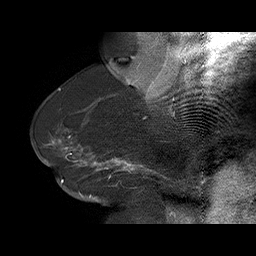
Breast MRI (dynamic contrast-enhanced), one sagittal slice; position 44 of 75 along the scan axis; dynamic contrast-enhanced series, time point 2 of 6 at this slice position (early post-contrast); 1.5 T; TE 4.5 ms, TR 32.4 ms; 256 × 256 image matrix. Female patient. From the clinical record (not read from this slice): setting: breast cancer imaged before/during neoadjuvant chemotherapy; receptor status: HR-positive, HER2-negative.
Structures marked on this image (semi-automatic segmentation, software-assisted and operator-edited):
- analysis volume of interest (the breast-tissue region the enhancement analysis was run in; not a lesion): bounding box [x1, y1, x2, y2] px = [58, 134, 166, 191]
- tumour enhancement mask (voxels above the 100 % enhancement threshold inside the analysis volume of interest): [58, 141, 150, 182]